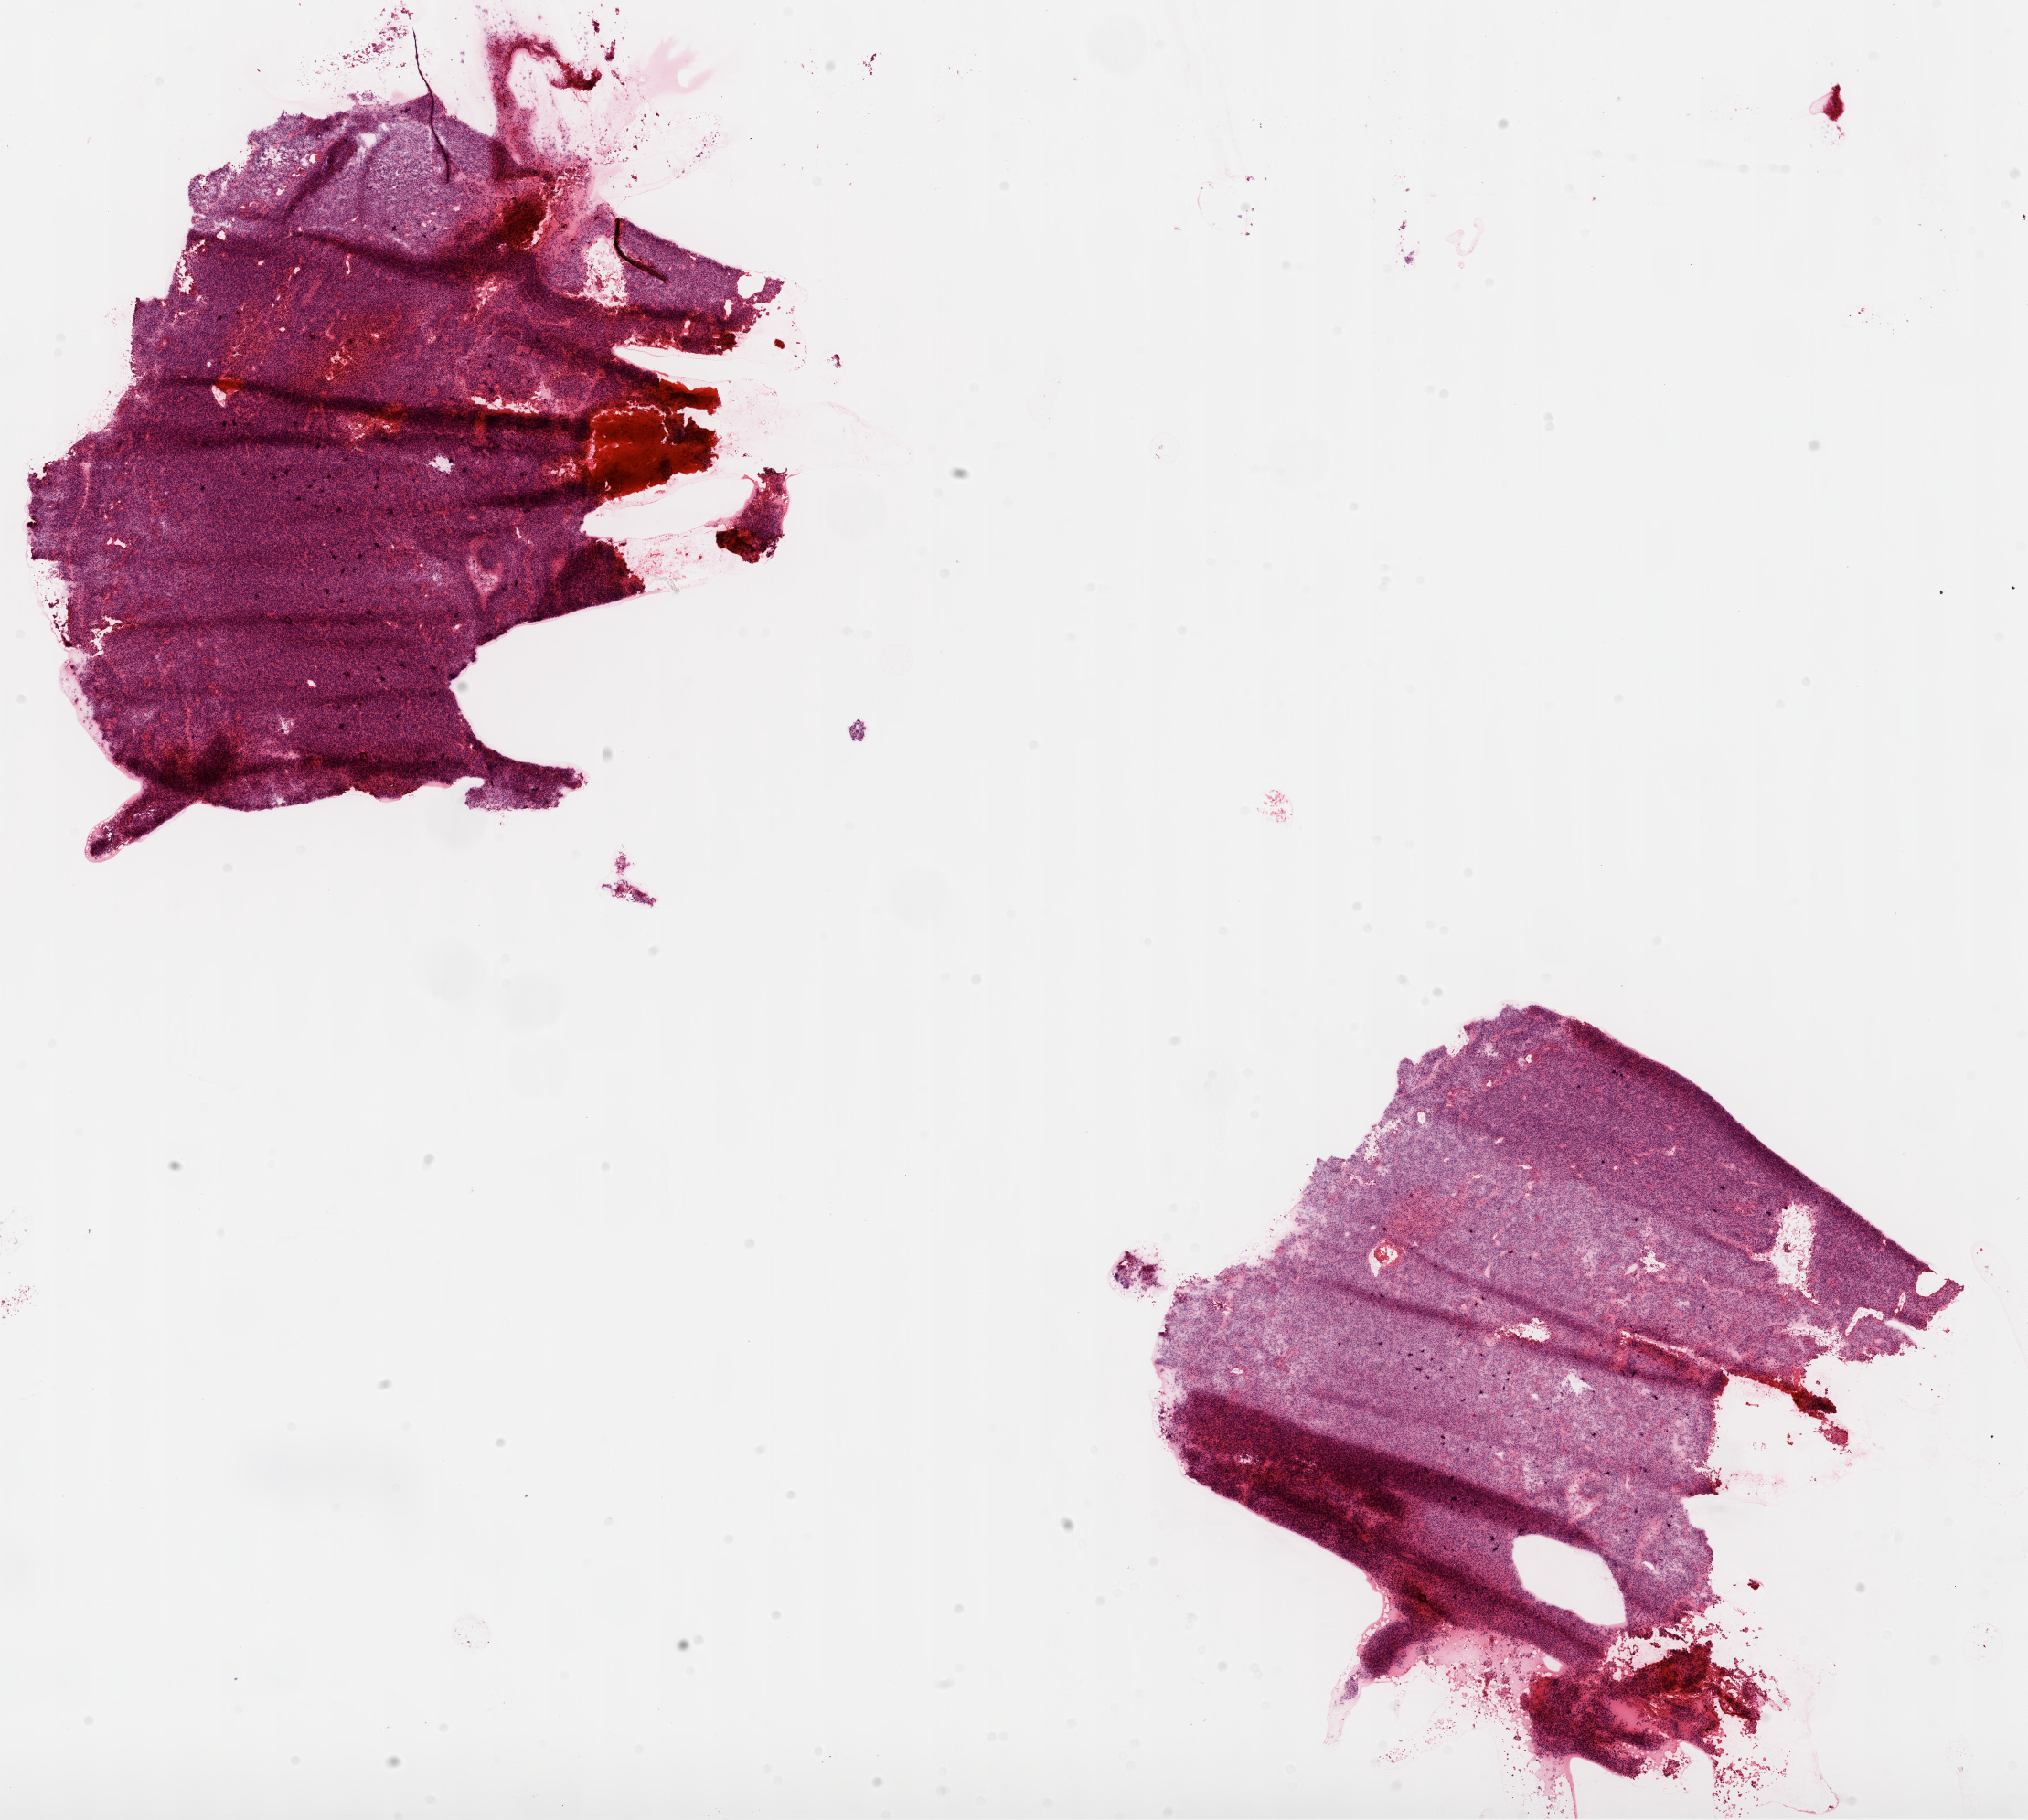
Whole-slide histology image, H&E-stained — a low-resolution overview of the entire scanned area, about 17.9 x 16.1 mm (acquisition: 20x scan); frozen section from the top of the tissue portion; sample: primary tumour, brain. Patient: female, age at initial diagnosis 31 years.
Histologic diagnosis: Glioblastoma.